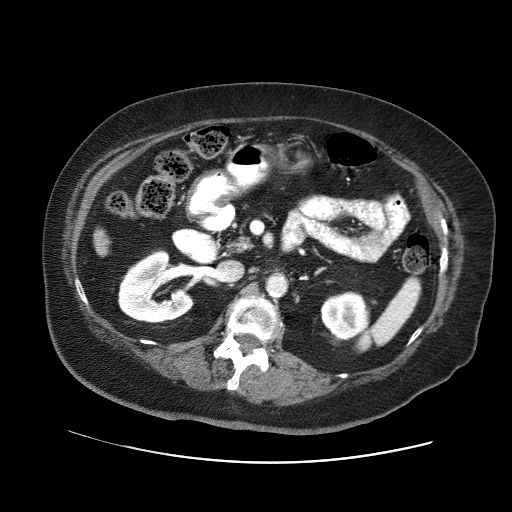
Contrast-enhanced abdominal CT (liver protocol), one axial slice; slice 9 of 71 in the series (ordered by position); reconstruction kernel STANDARD; soft-tissue window (W 400 / L 40 HU); 2.5 mm slice thickness; 512 × 512 image matrix, field of view 400 × 400 mm. From the clinical record (not read from this slice): diagnosis: hepatocellular carcinoma (patient treated with transarterial chemoembolisation; whether this scan precedes or follows treatment is not stated here); TNM stage (as recorded): Stage-II; Child-Pugh class: A; tumour differentiation: poorly differentiated; tumour nodularity: multinodular.
Annotated regions visible in this slice (semi-automatically segmented with operator editing):
- liver parenchyma outside the tumour (the mass and vessels are separate outlines, so this box may not span the whole liver): box from (x=94, y=230) to (x=108, y=254) px